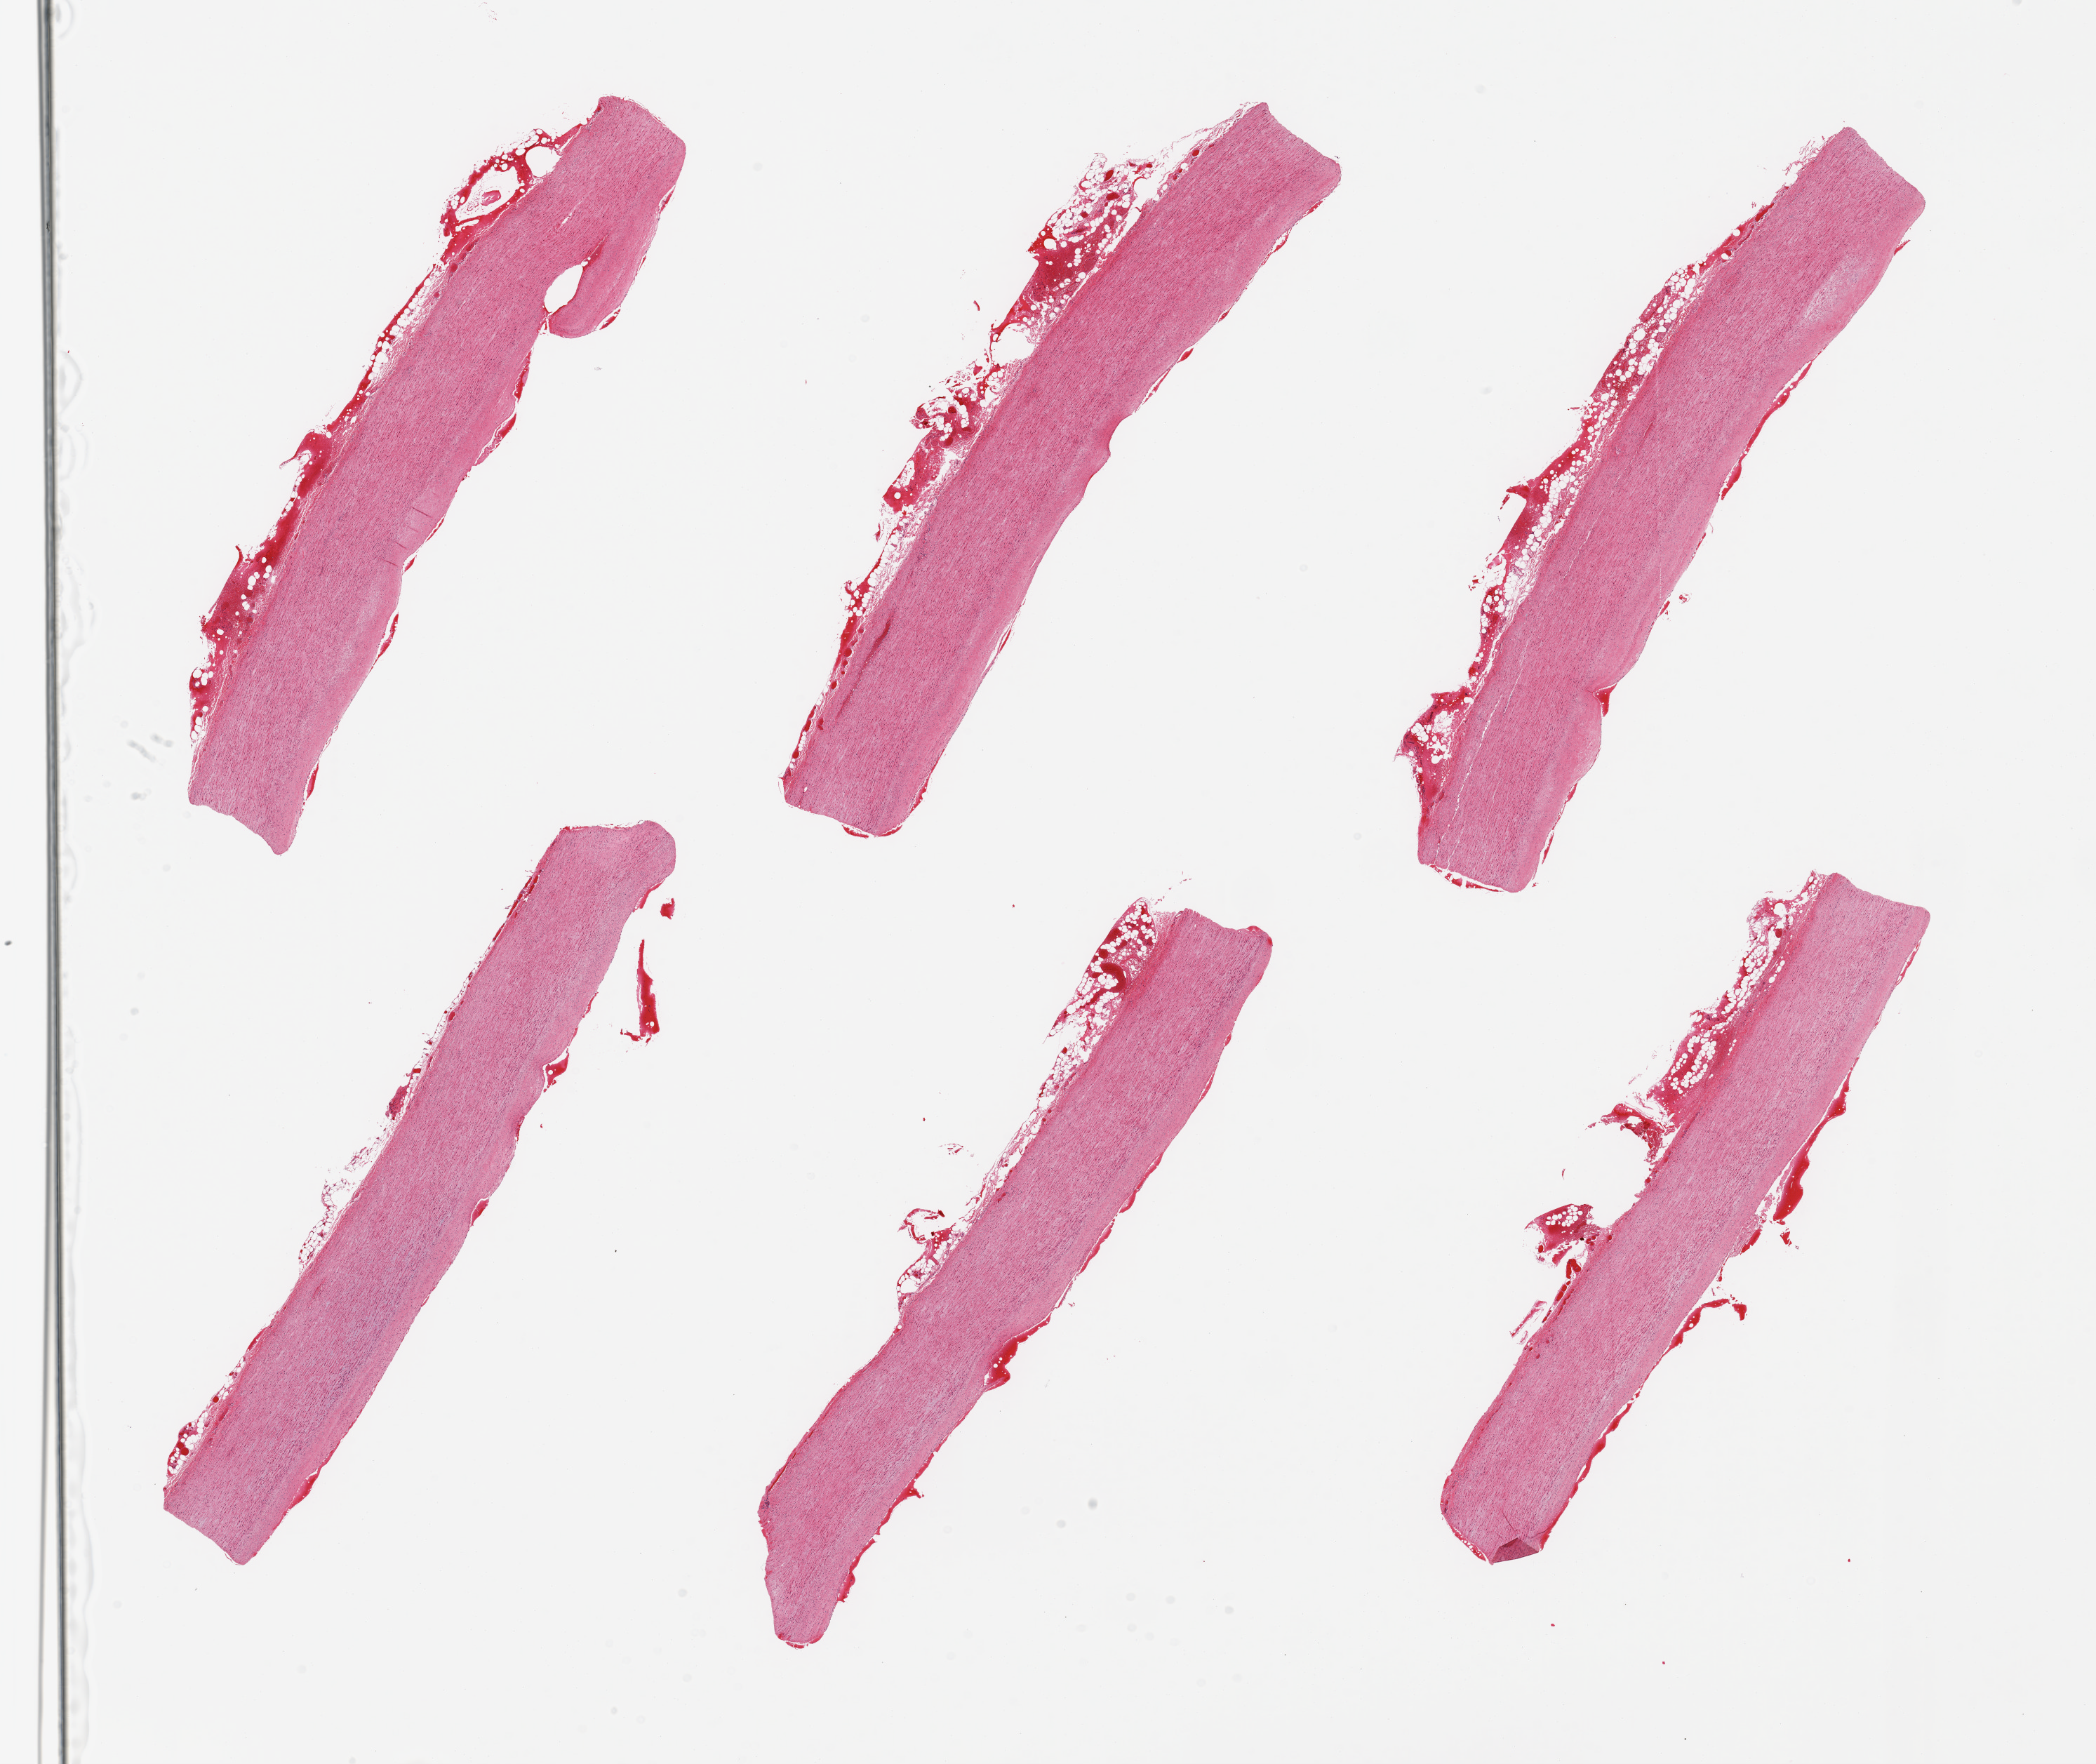
Digitized hematoxylin and eosin (H&E)-stained section, shown as a low-resolution overview of the whole scanned area (about 23.6 x 19.9 mm, acquisition: 20x scan); PAXgene-fixed paraffin-embedded (PFPE) section; section of aorta (target tissue); donor tissue sample.
Pathologist's review note for this sample: 6 pieces, minimal atherosis.